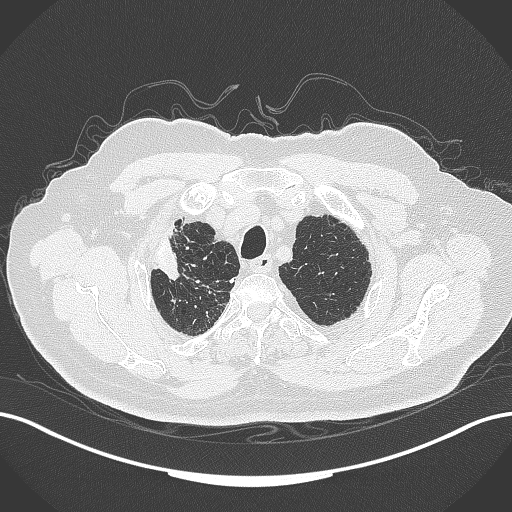
Chest CT, one axial slice; position 310 of 389 along the scan axis; reconstruction kernel B70f; 120 kVp; lung window (W 1500 / L -600 HU); 1 mm slice thickness; 512 × 512 image matrix, field of view 400 × 400 mm. Male patient, age 72 years. From the clinical record (not read from this slice): clinical TNM (as recorded): T1a N0 M0.
Outlined on this slice (bounding box drawn by a radiologist):
- lung tumour (recorded histology: squamous cell carcinoma): bounding box (x1, y1, x2, y2) in pixels: (151, 231, 187, 288)